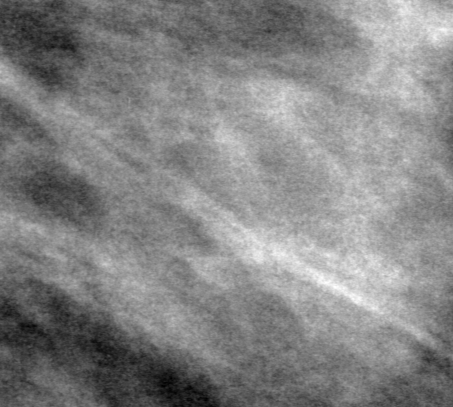
Cropped region of a digitized screen-film mammogram centred on a radiologist-marked abnormality, left breast, MLO view.
Finding: mass, shape oval, margins obscured; BI-RADS assessment category 0 (incomplete: needs additional imaging); pathology (as recorded): benign.